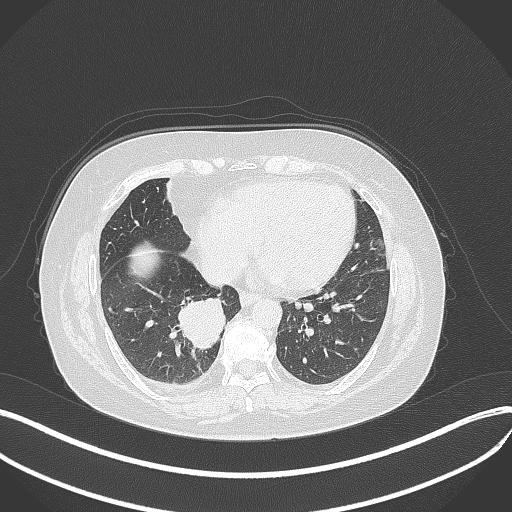
Chest CT, one axial slice; slice 126 of 381 in the series (ordered by position); lung window (W 1500 / L -600 HU); 1 mm slice thickness; 512 × 512 image matrix, field of view 400 × 400 mm. Female patient, age 56 years. From the clinical record (not read from this slice): clinical TNM (as recorded): T2b N1 M0.
Annotated regions visible in this slice (bounding box drawn by a radiologist):
- lung tumour (recorded histology: small cell carcinoma): box from (x=173, y=289) to (x=227, y=352) px